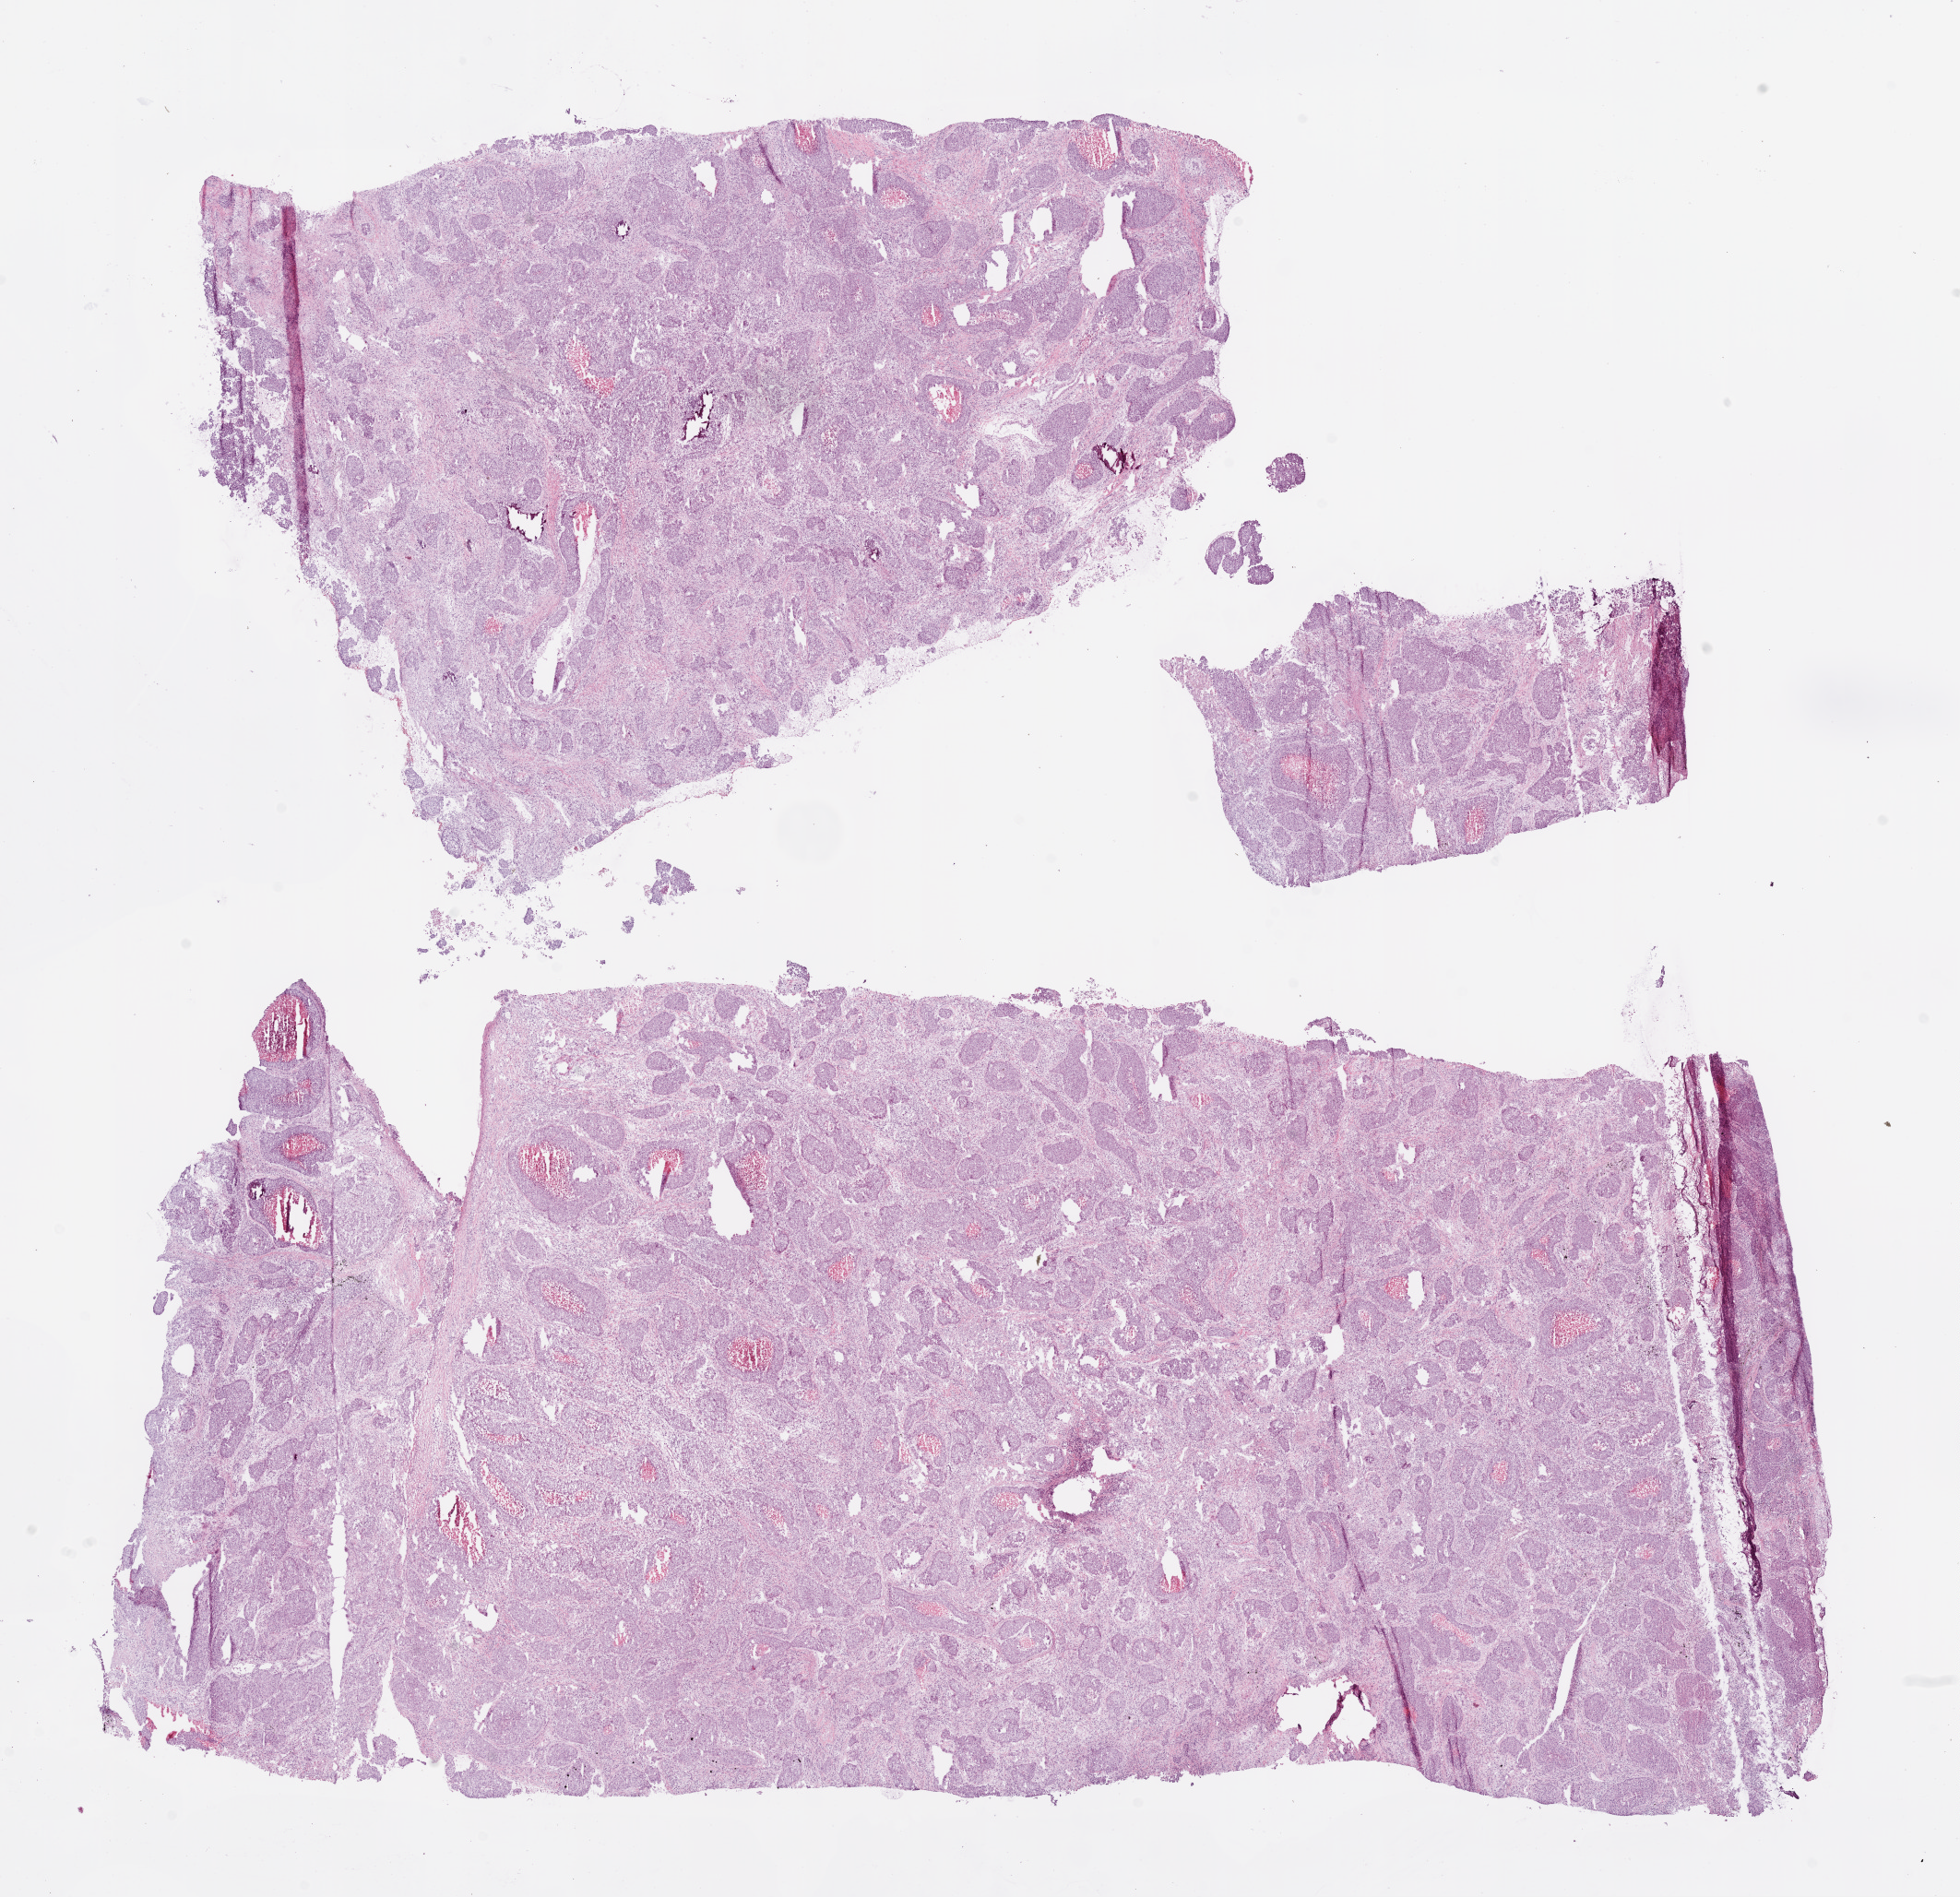
Digitized H&E-stained tissue section (whole slide), low-resolution overview of the scanned area, about 17.1 x 16.5 mm. Frozen section from the bottom of the tissue portion. Sample: primary tumour, lung. Female patient; age at initial diagnosis 73 years. Slide review estimates, as recorded: tumour cells 60%, tumour nuclei 65%, normal cells 0%, stromal cells 30%, necrosis 10%.
Pathologic diagnosis: Squamous cell carcinoma, NOS (upper lobe, lung). AJCC pathologic stage: IIB.